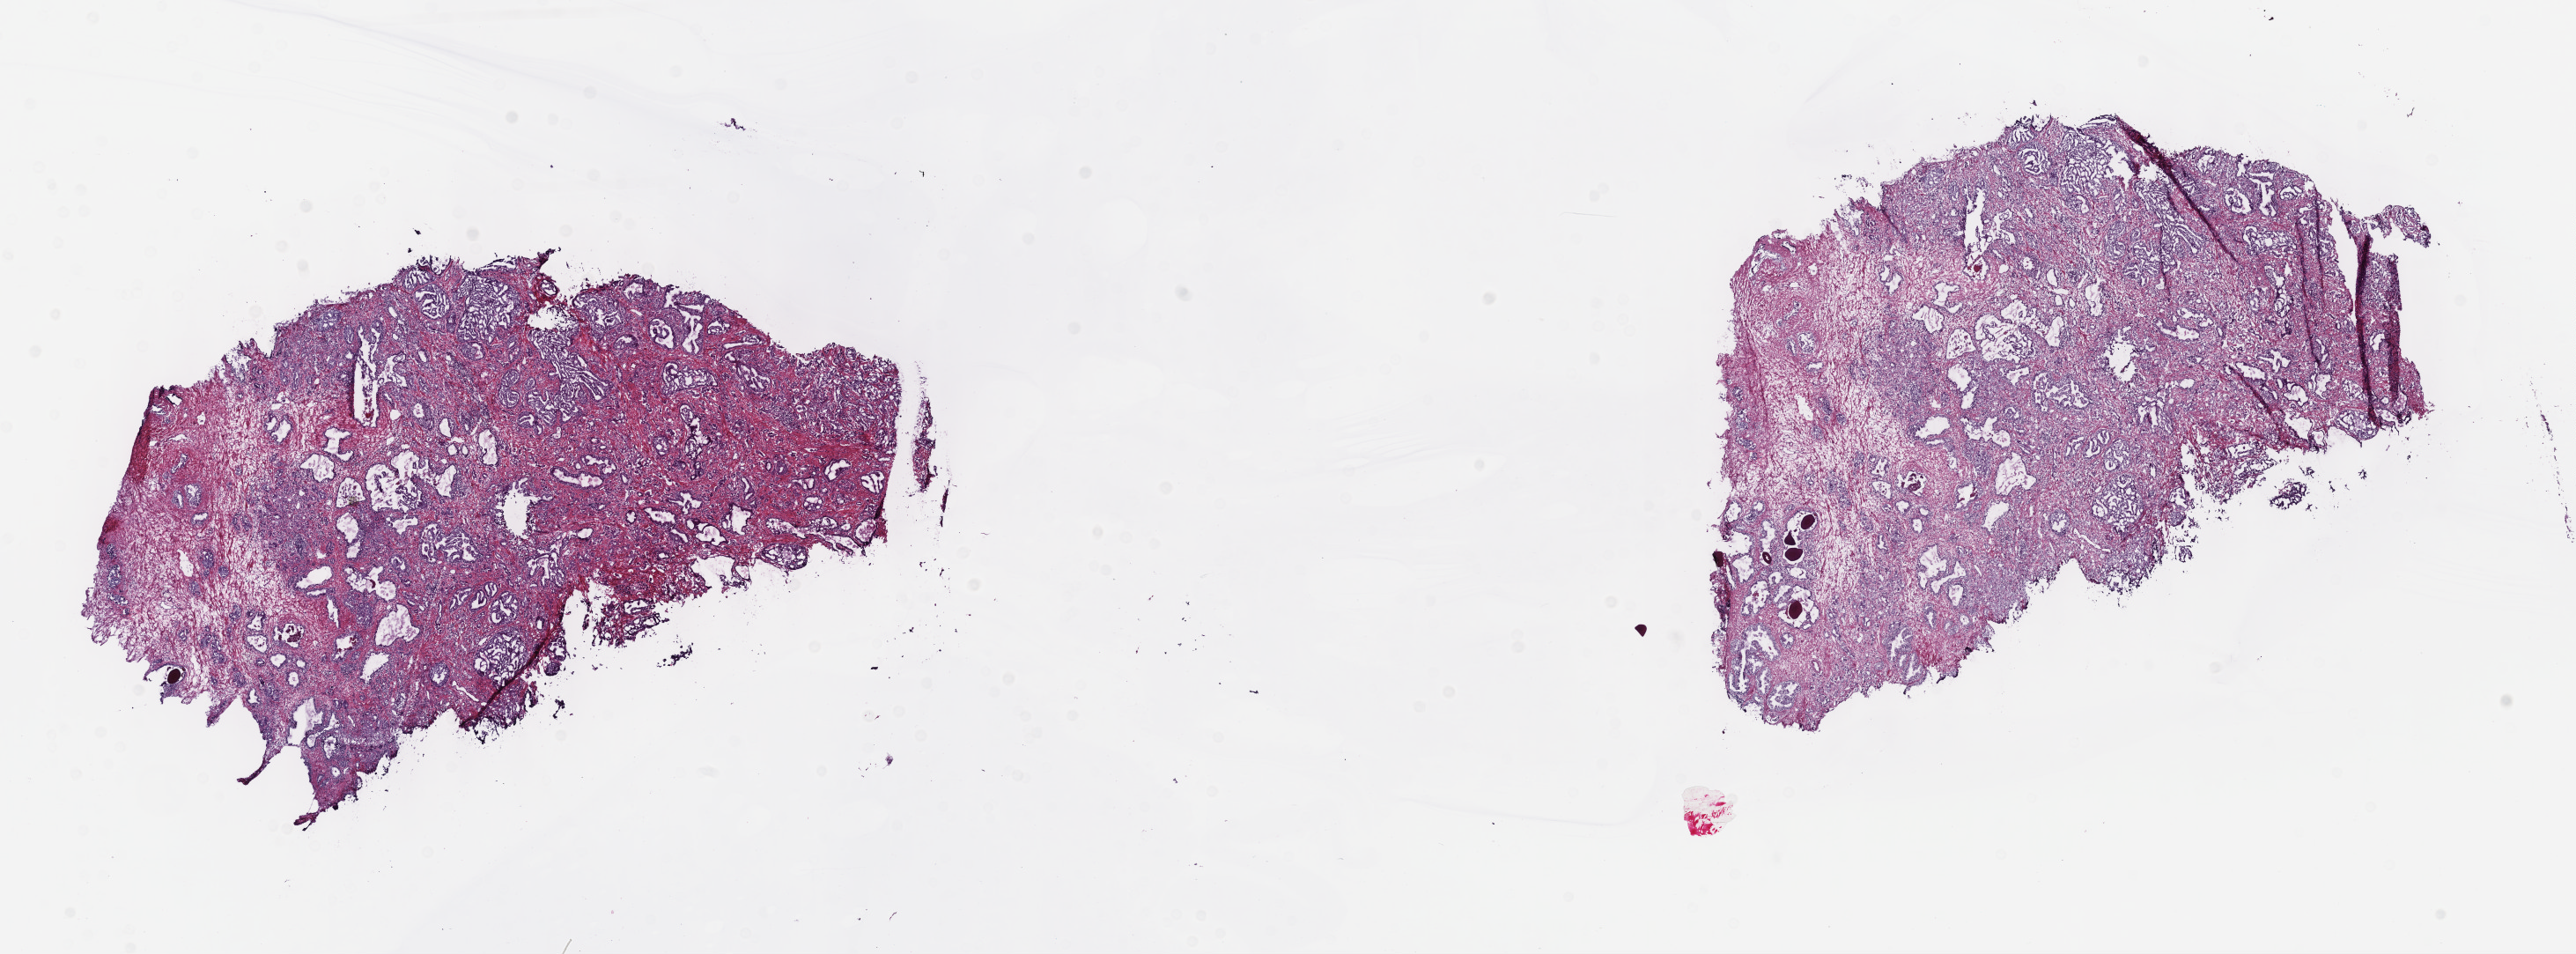
Hematoxylin and eosin (H&E) stained whole-slide image — a low-resolution overview of the entire scanned area, about 23.7 x 8.8 mm (slide scanned at 40x), frozen section from the top of the tissue portion, sample: primary tumour, prostate. Patient: male, age at initial diagnosis 55 years. Pathologist review of this section (percent, as recorded): tumour cells 42%, tumour nuclei 75%.
Pathologic diagnosis: Adenocarcinoma, NOS (prostate gland).